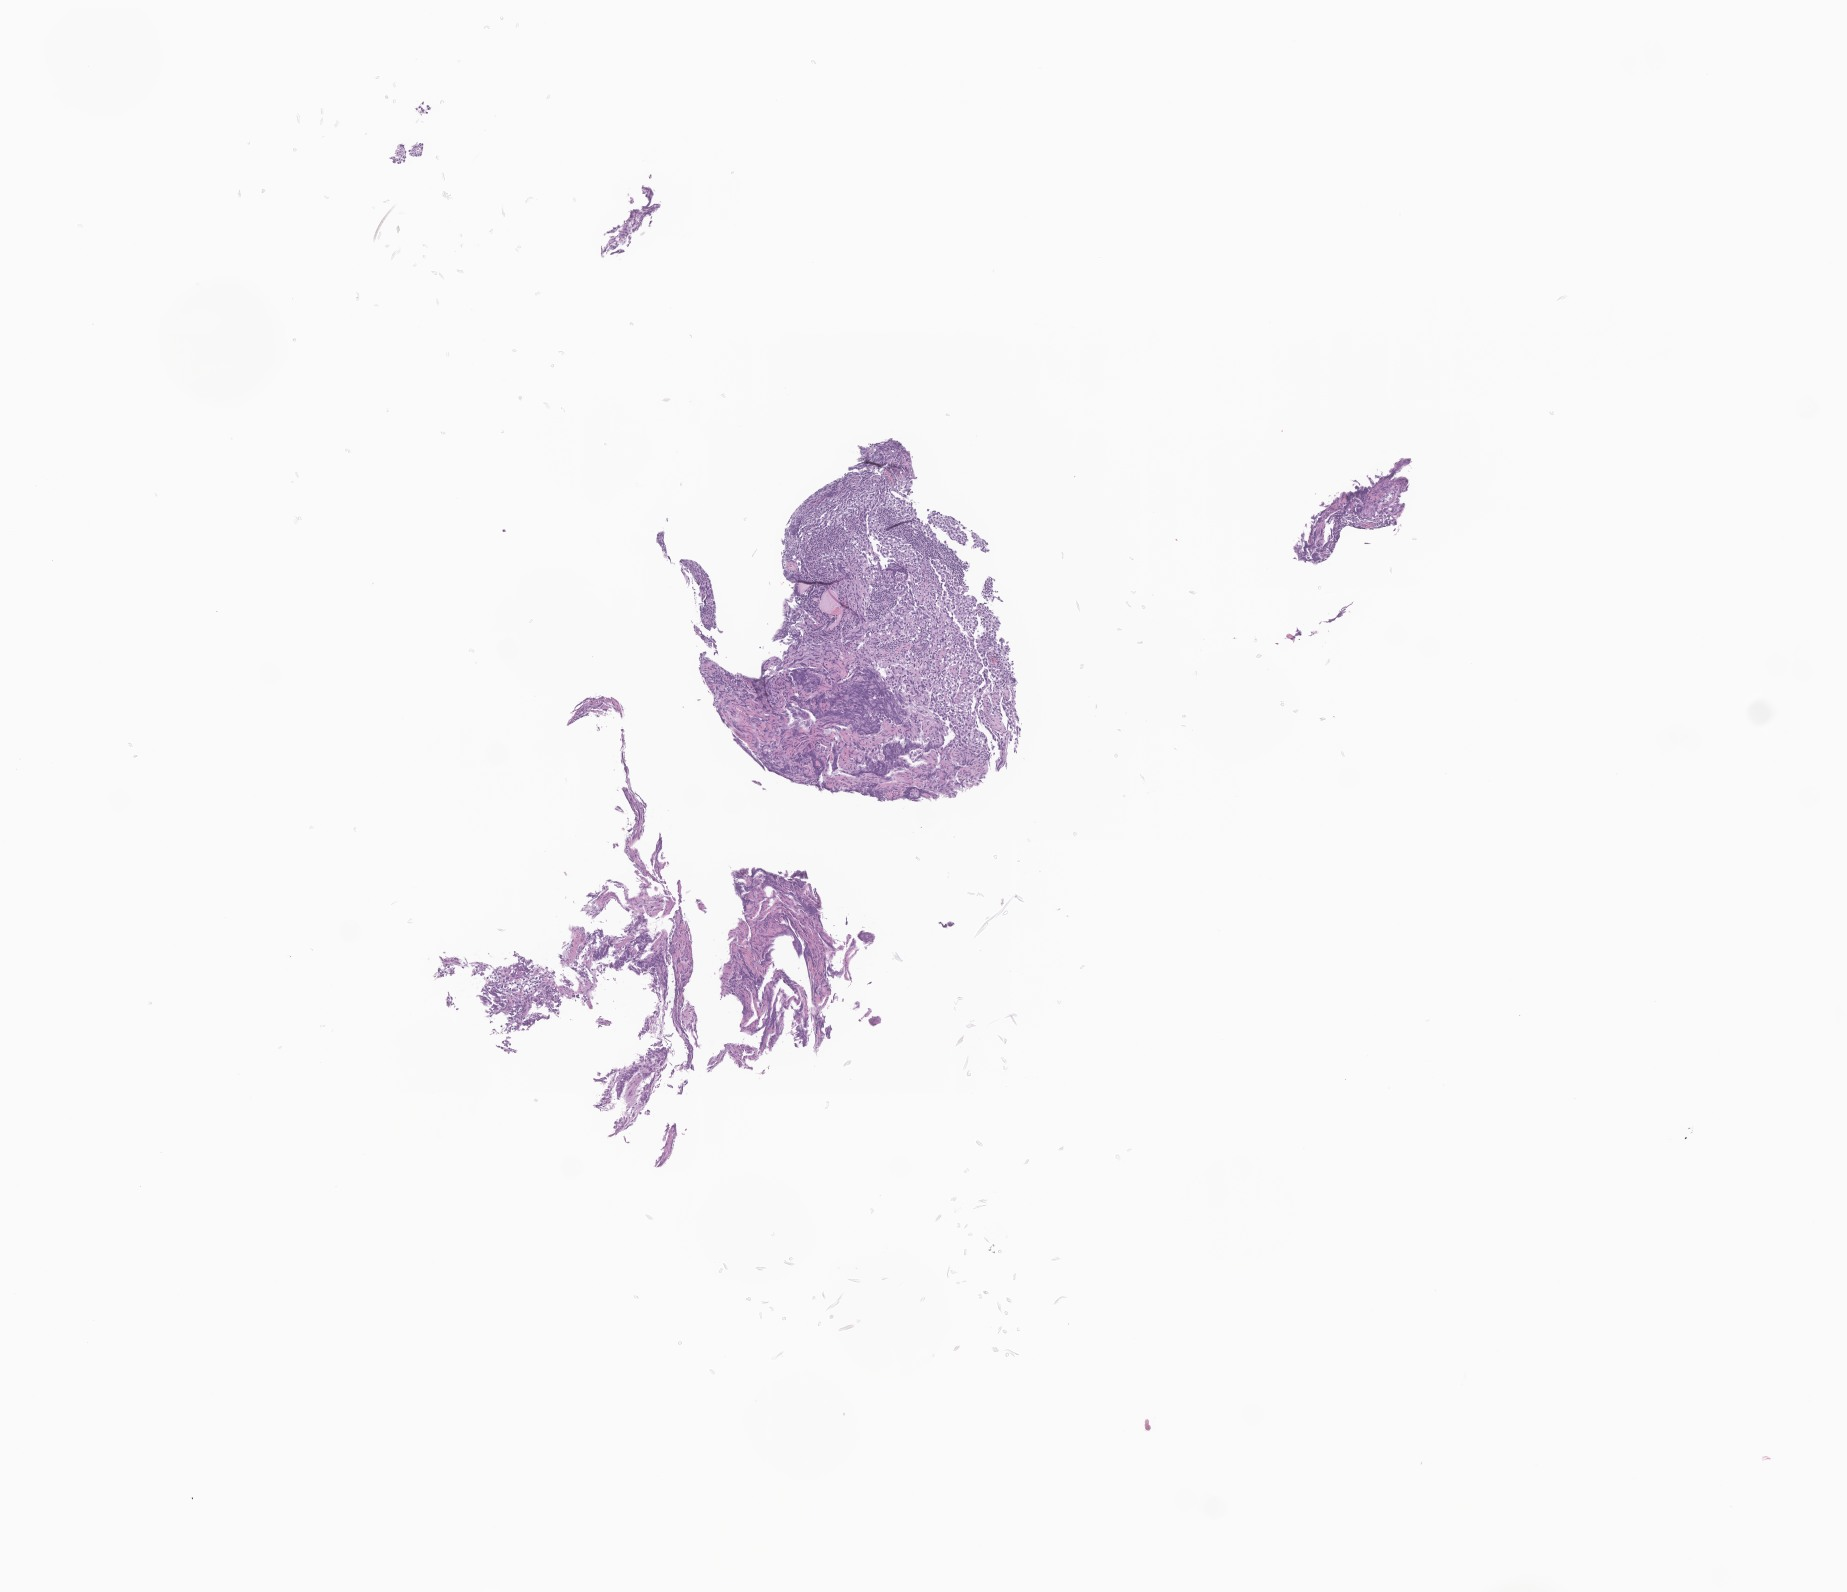
Whole-slide image, haematoxylin and eosin stain of tumor tissue from the brain — a low-resolution overview of the entire scanned area, about 7.8 x 6.7 mm. Formalin-fixed, paraffin-embedded (FFPE) tissue. Patient male; age 246 months (20 years 6 months).
Diagnosis (ICD-O-3 morphology term): Neoplasm, malignant.